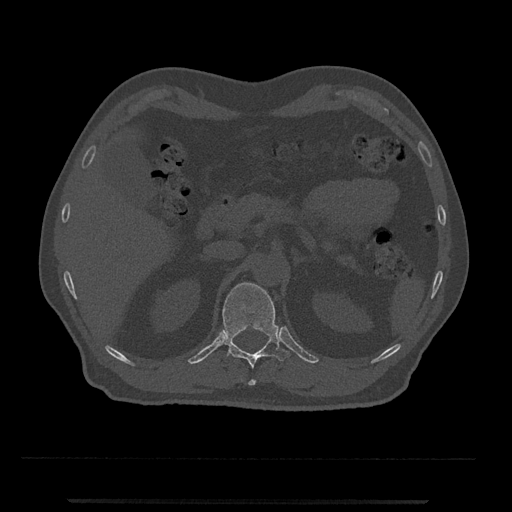
CT including the spine, one axial slice; bone window (W 1800 / L 400 HU); 0.5 mm slice thickness; 512 × 512 image matrix. Patient: male, 63 years. Case-level facts recorded for this patient, not image findings: primary cancer: prostate.
Annotated regions visible in this slice (semi-automatic segmentation, software-assisted and operator-edited):
- T12 vertebra: bounding box (x1, y1, x2, y2) in pixels: (221, 282, 289, 386)